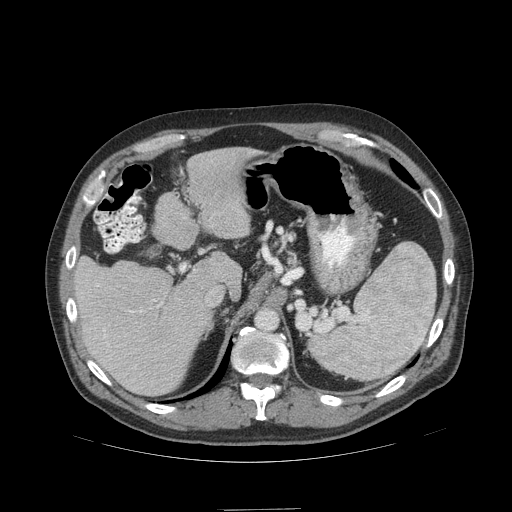
Contrast-enhanced abdominal CT (liver protocol), one axial slice. Position 70 of 99 along the scan axis. 140 kVp. Soft-tissue window (W 400 / L 40 HU). 2.5 mm slice thickness. 512 × 512 image matrix. From the clinical record (not read from this slice): diagnosis: hepatocellular carcinoma (patient treated with transarterial chemoembolisation; whether this scan precedes or follows treatment is not stated here); TNM stage (as recorded): Stage-I; Child-Pugh class: A; tumour differentiation: no biopsy; tumour nodularity: uninodular.
Annotated regions visible in this slice (semi-automatic segmentation, software-assisted and operator-edited):
- liver parenchyma outside the tumour (the mass and vessels are separate outlines, so this box may not span the whole liver): bounding box (x1, y1, x2, y2) in pixels: (74, 148, 258, 396)
- liver vessels: (96, 284, 208, 367)